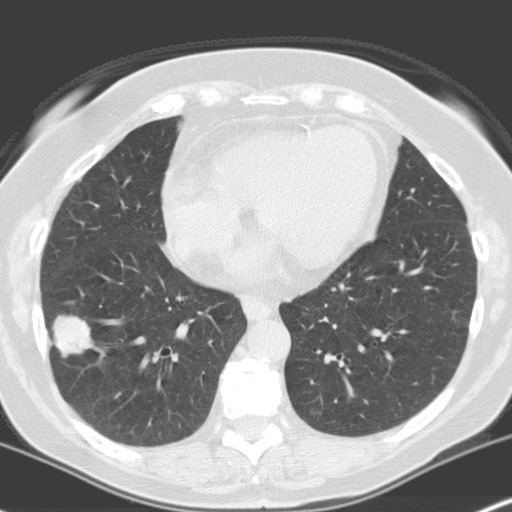
Chest CT (low-dose screening protocol), one axial image, baseline screening round, lung window (W 1500 / L -600 HU), slice 93 of 160 in the series, 512 × 512 image matrix, field of view 316 × 316 mm. Female participant, aged 70 years at enrolment. Current smoker at enrolment.
Lesion marked by an expert reader, bounding box <33,304,100,373> (left, top, right, bottom; pixels). The screening reader recorded 4 non-calcified nodules or masses ≥4 mm on this exam; which of them this box marks is not recorded. Participant outcome: lung cancer diagnosed 28 days after this screen — adenocarcinoma, NOS, right lower lobe, moderately differentiated (G2), stage IV (AJCC 6th edition), 28 mm at pathology.